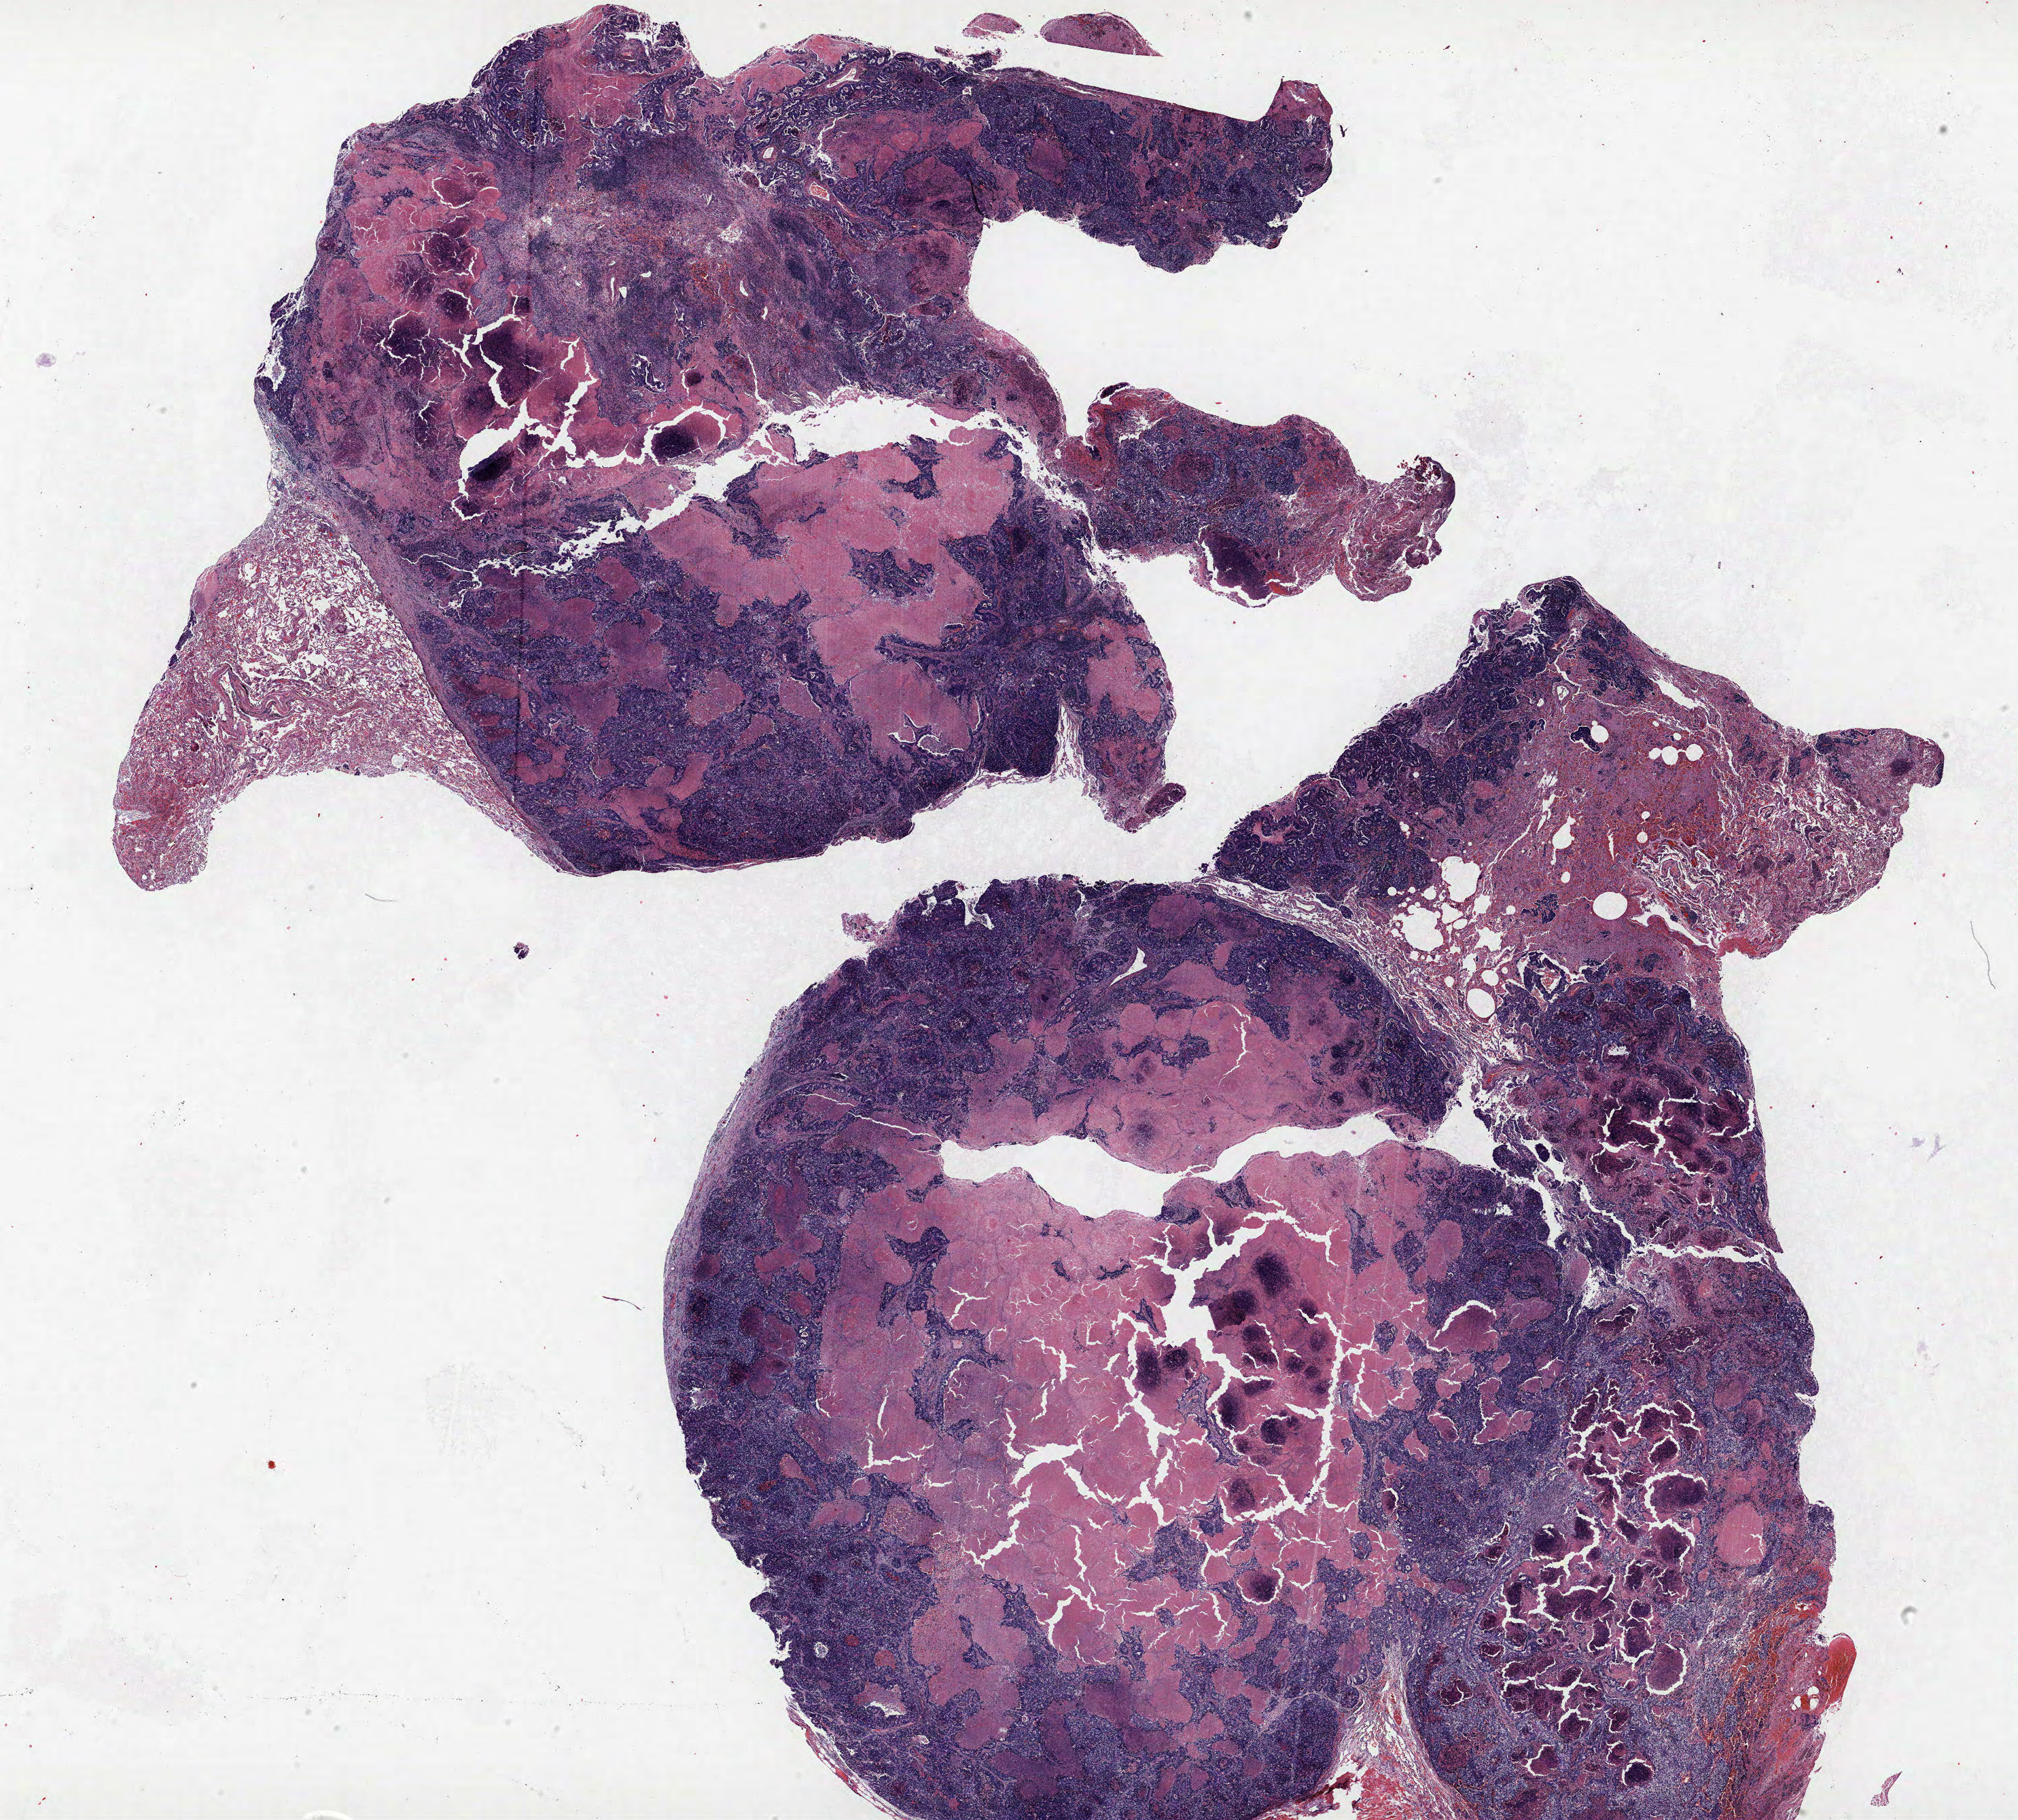
Whole-slide histology image, H&E, low-resolution overview of the scanned area, about 23.8 x 21.4 mm (acquisition: 40x scan). FFPE section. Lung. Male patient, aged 60 at enrolment. Current smoker at enrolment. Grade: undifferentiated (G4).
Participant's lung-cancer diagnosis: Large cell carcinoma, NOS (ICD-O-3 8012/3). Primary tumour location (clinical record): right lower lobe. ICD-O-3 topography: lower lobe of lung (C34.3). Stage (AJCC 6th edition): IA. Tumour size (pathology): 16 mm.